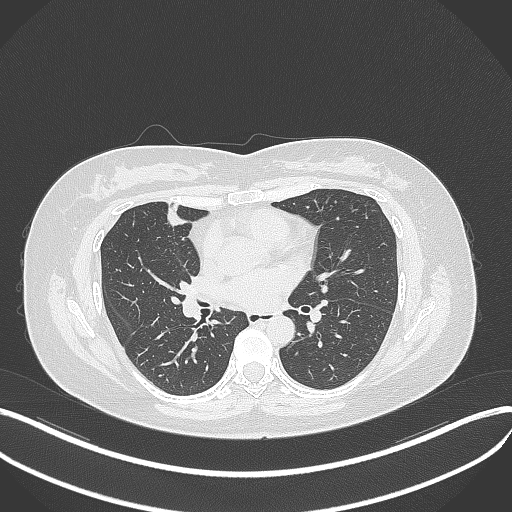
Chest CT, one axial slice; position 161 of 273 along the scan axis; reconstruction kernel B70f; lung window (W 1500 / L -600 HU); 1 mm slice thickness; 512 × 512 image matrix, field of view 400 × 400 mm. Patient: female, 42 years. From the clinical record (not read from this slice): clinical TNM (as recorded): T1b N0 M0.
Structures marked on this image (rectangle marked by the reading radiologist):
- lung tumour (recorded histology: adenocarcinoma): bounding box <159,204,186,230> (left, top, right, bottom; pixels)